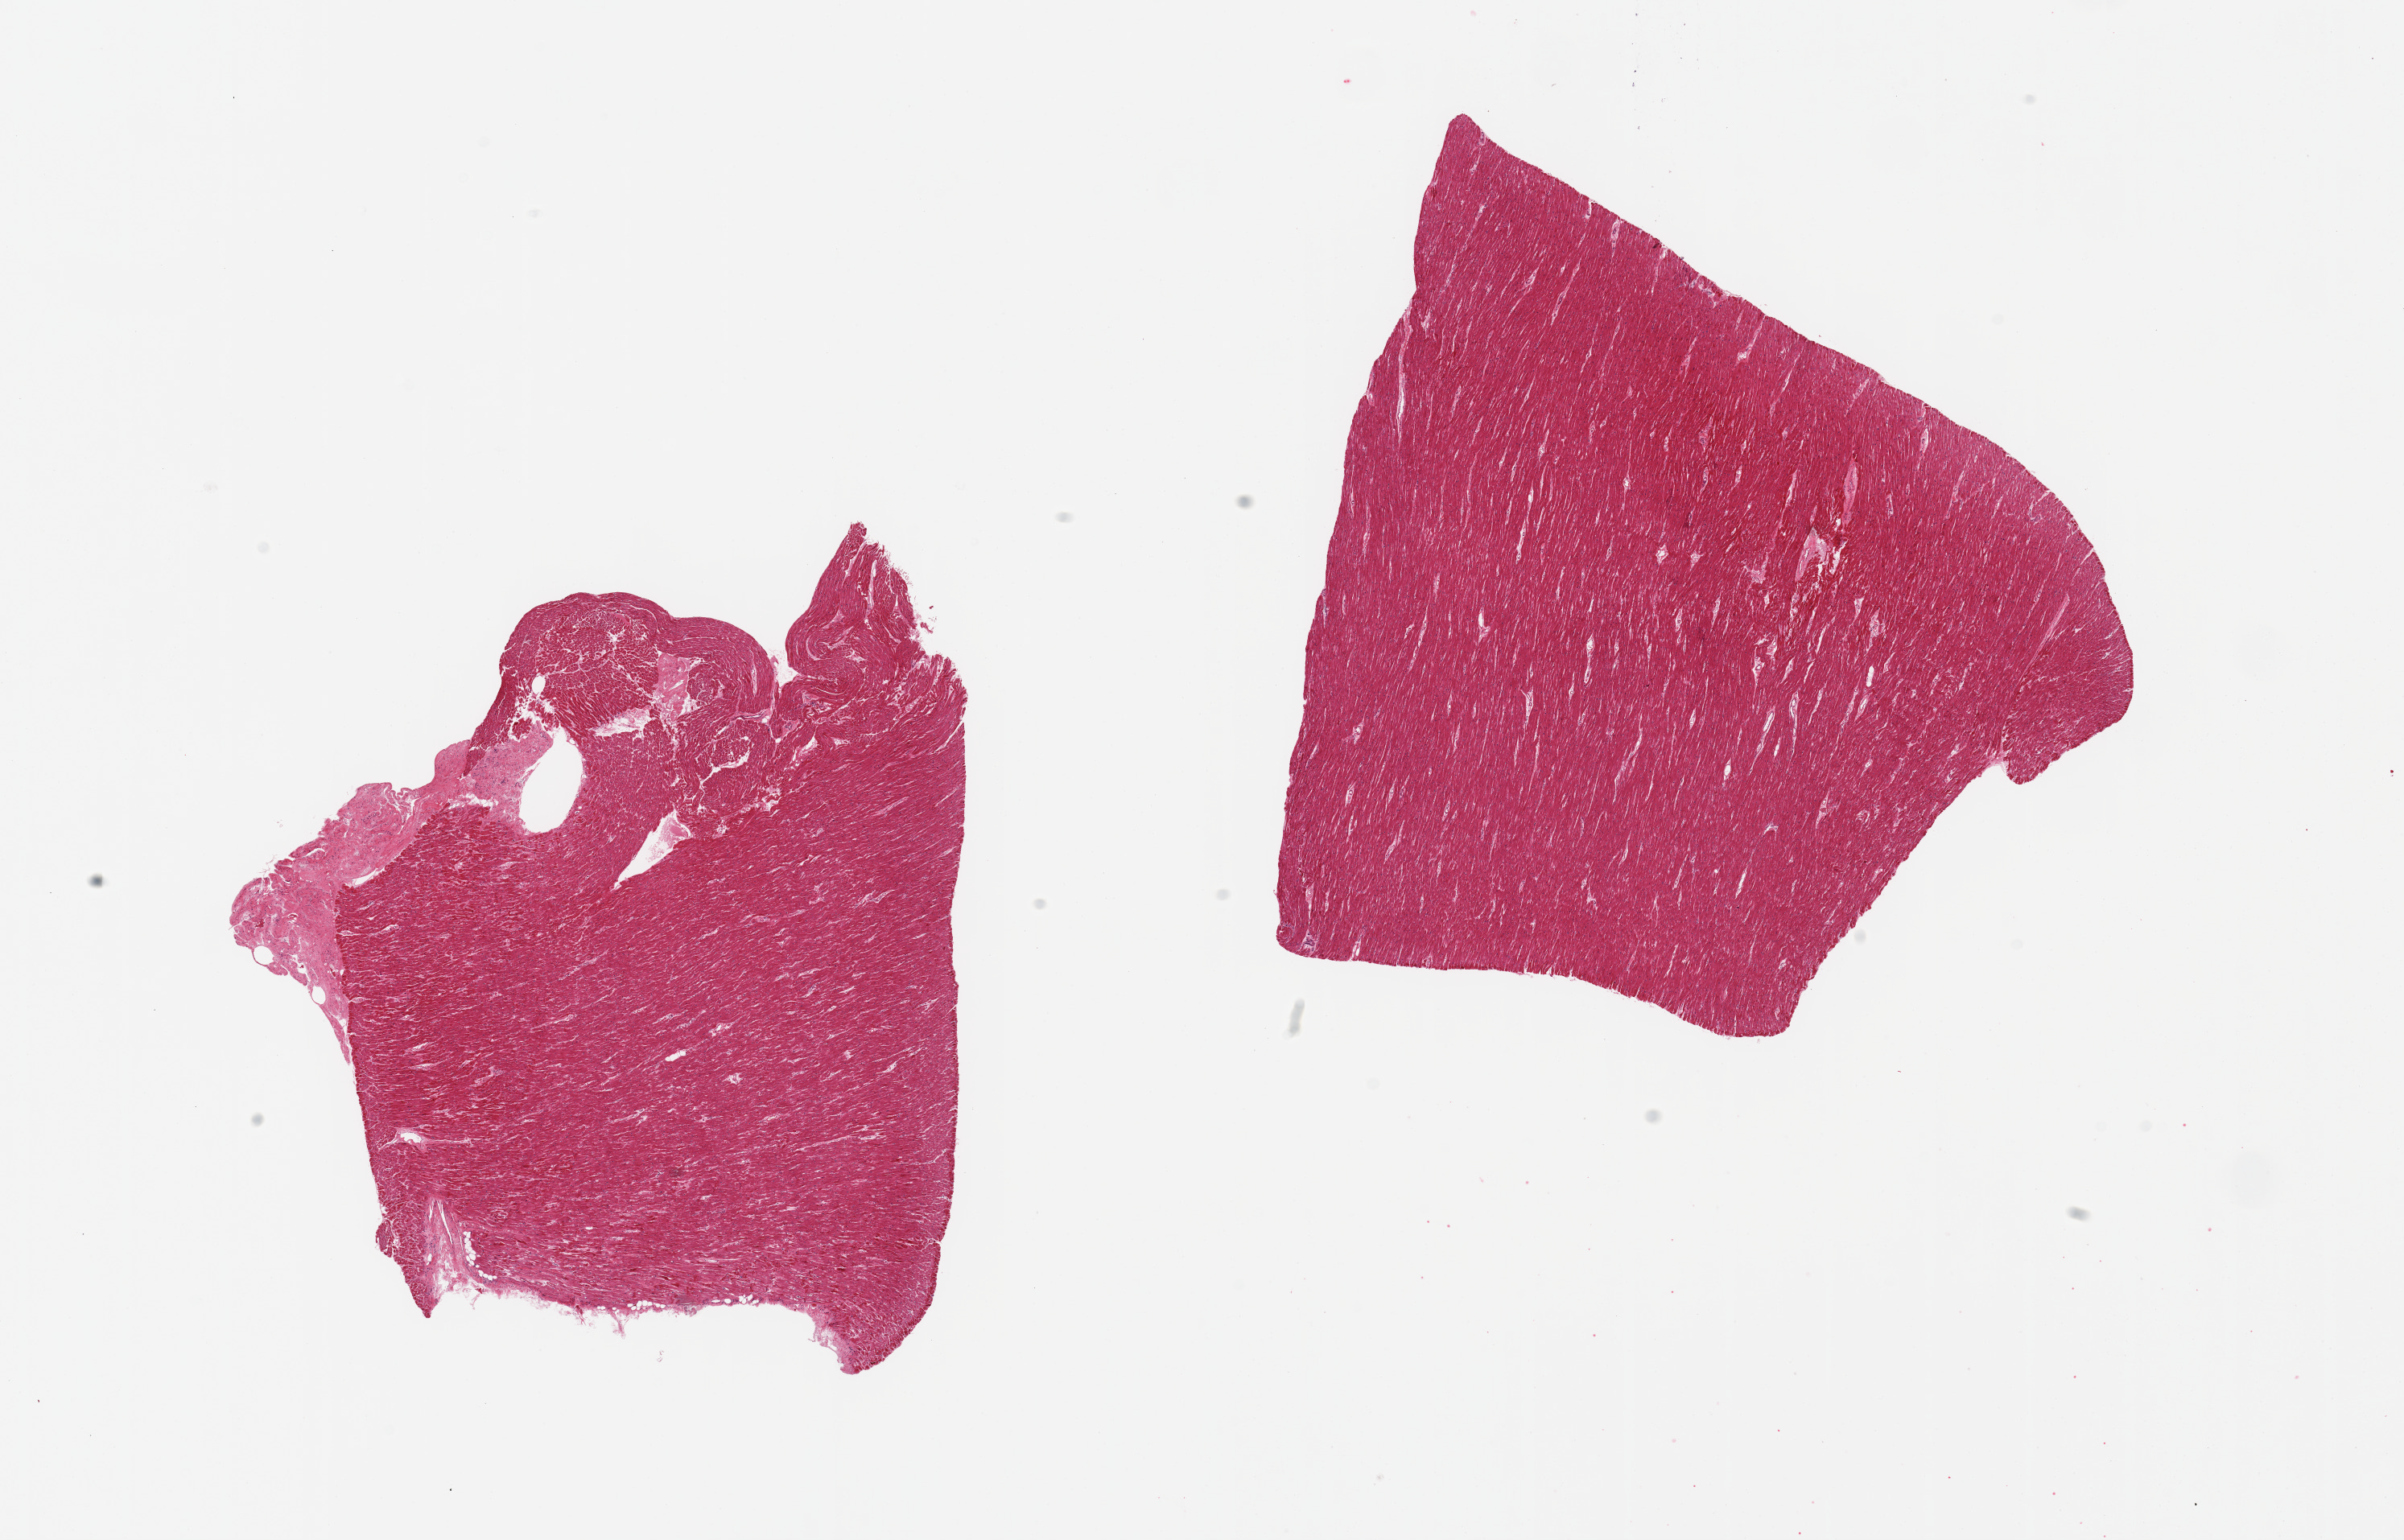
H&E whole-slide image, low-resolution overview of the scanned area, about 23.6 x 15.1 mm. PAXgene-fixed, paraffin-embedded tissue. Target tissue: heart. Donor tissue sample. Donor: male.
Pathologist's review note for this sample: 2 pieces, minimal interstitial fibrosis.